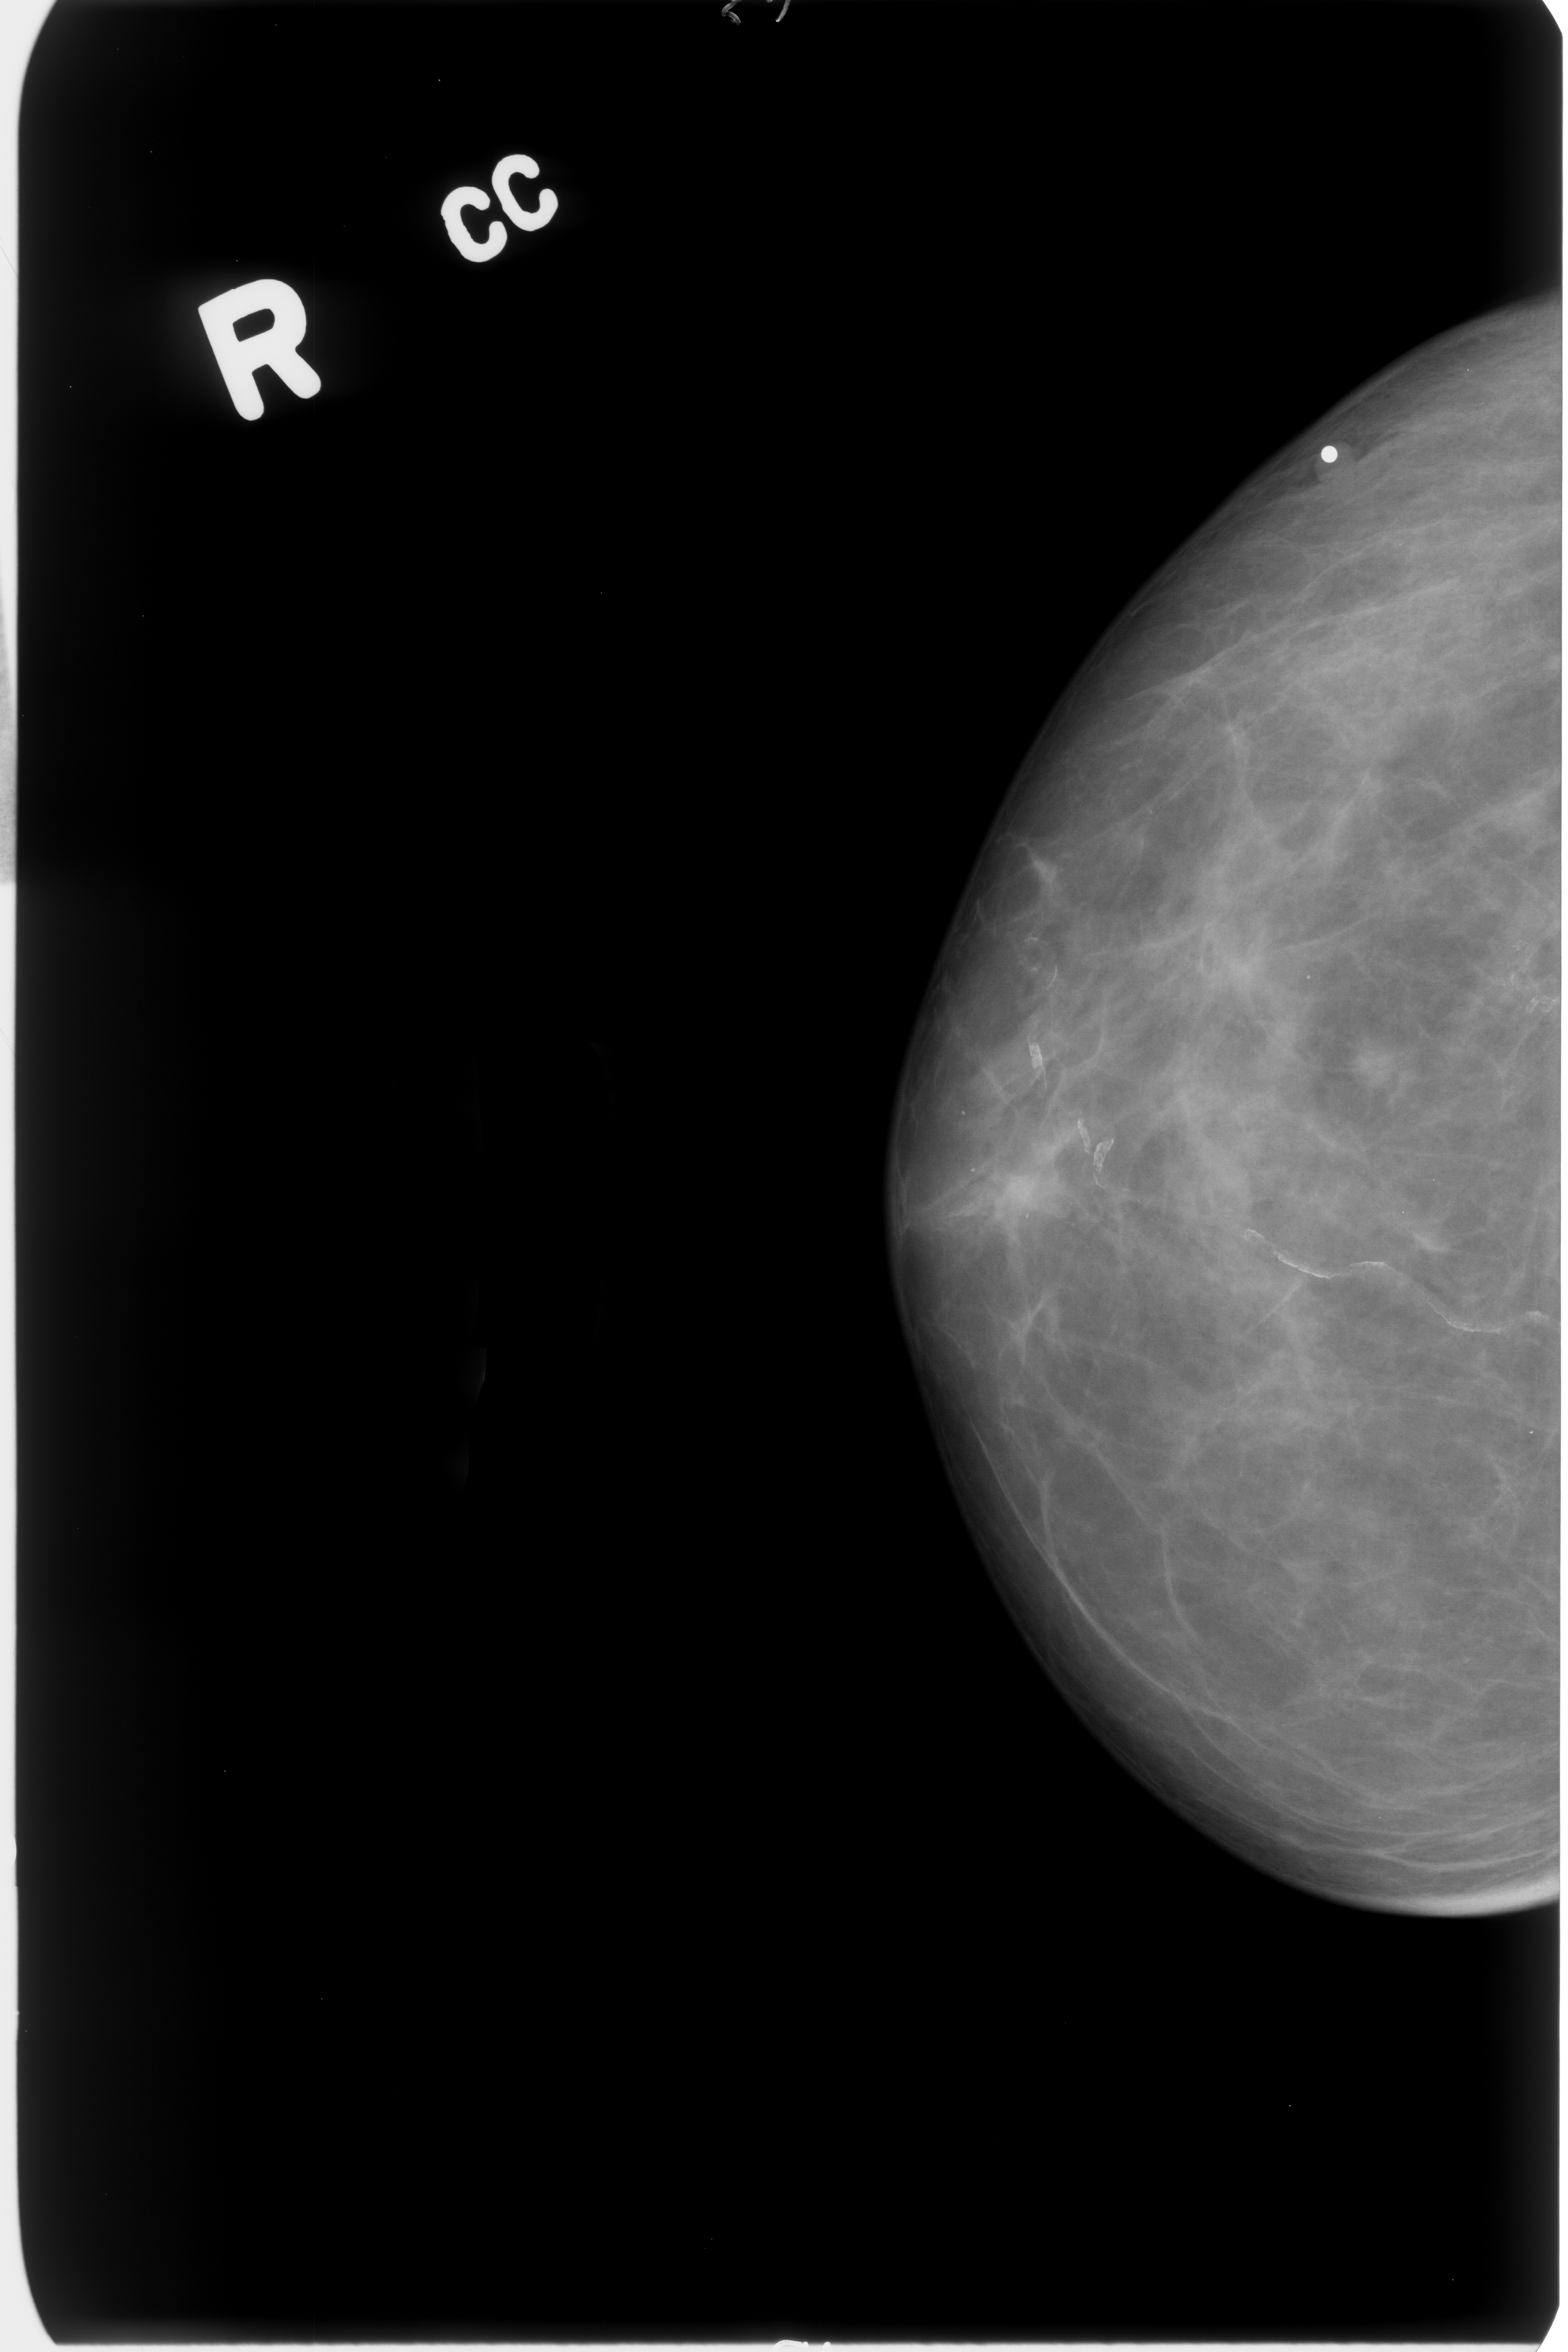
Mammogram (digitized film); right breast; craniocaudal (CC) view; breast composition: scattered fibroglandular densities (BI-RADS density category 2 of 4).
- Finding: calcifications, morphology vascular; BI-RADS assessment category 2; subtlety rating 4 on a 1 (subtle) to 5 (obvious) scale; benign; no additional work-up was recommended (benign without callback).